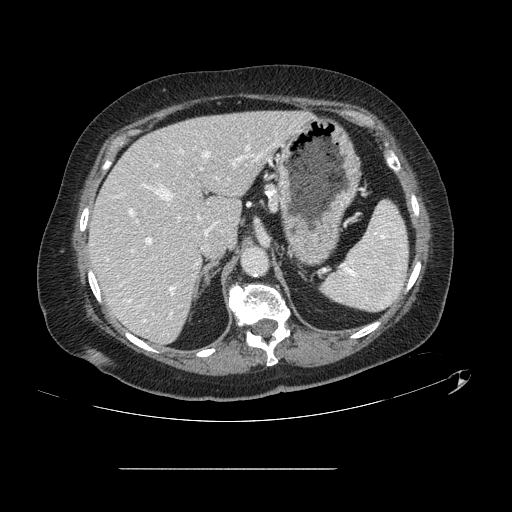
Contrast-enhanced abdominal CT, one axial slice. Position 88 of 148 along the scan axis. Soft-tissue window (W 400 / L 40 HU). 2.5 mm slice thickness. 512 × 512 image matrix, field of view 439 × 439 mm. Female patient, age 75 years. From the clinical record (not read from this slice): diagnosis: colorectal cancer liver metastases, imaged before liver resection; multiple liver metastases: no; largest metastasis: 2.4 cm; disease in both lobes: no.
Annotated regions visible in this slice (outlined manually by an expert reader):
- hepatic veins: bounding box (x1, y1, x2, y2) in pixels: (129, 151, 209, 322)
- liver: (90, 112, 308, 343)
- planned liver remnant (the part of the liver to remain after resection): (90, 112, 308, 343)
- portal vein (with intrahepatic branches): (129, 145, 263, 292)